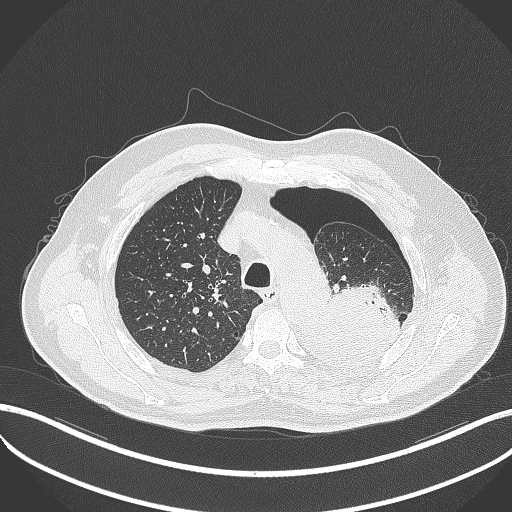
Chest CT, one axial slice. Slice 387 of 464 in the series (ordered by position). 120 kVp. Lung window (W 1500 / L -600 HU). 1 mm slice thickness. 512 × 512 image matrix, field of view 400 × 400 mm. Male patient, age 76 years. Case-level facts recorded for this patient, not image findings: clinical TNM (as recorded): T3 N0 M1b.
Annotated regions visible in this slice (bounding box drawn by a radiologist):
- lung tumour (recorded histology: adenocarcinoma): box from (x=293, y=279) to (x=403, y=362) px